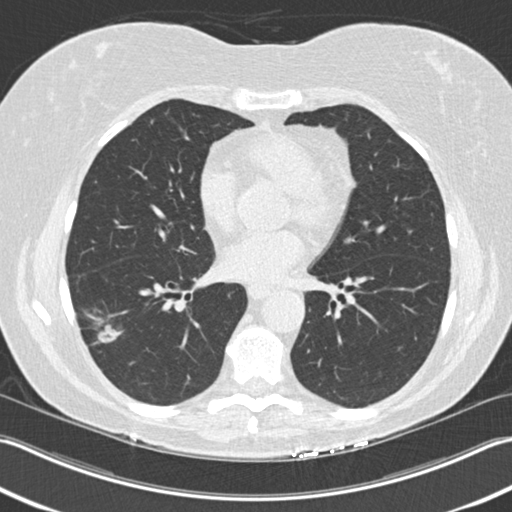
Axial slice from a low-dose chest CT screening exam, baseline screening round, lung window (W 1500 / L -600 HU), standard (soft-tissue) reconstruction kernel (B30f), slice 105 of 211 in the series, 512 × 512 image matrix, field of view 348 × 348 mm. Female participant, aged 63 years at enrolment. Current smoker at enrolment.
Expert reader's lesion annotation, box from (x=66, y=307) to (x=132, y=369) px. The screening reader recorded 3 non-calcified nodules or masses ≥4 mm on this exam (right upper lobe, right lower lobe, right lower lobe); which of them this box marks is not recorded. Lung cancer was diagnosed 57 days after this screen: bronchiolo-alveolar adenocarcinoma, NOS, right lower lobe, well differentiated (G1), stage IA (AJCC 6th edition), 25 mm at pathology.